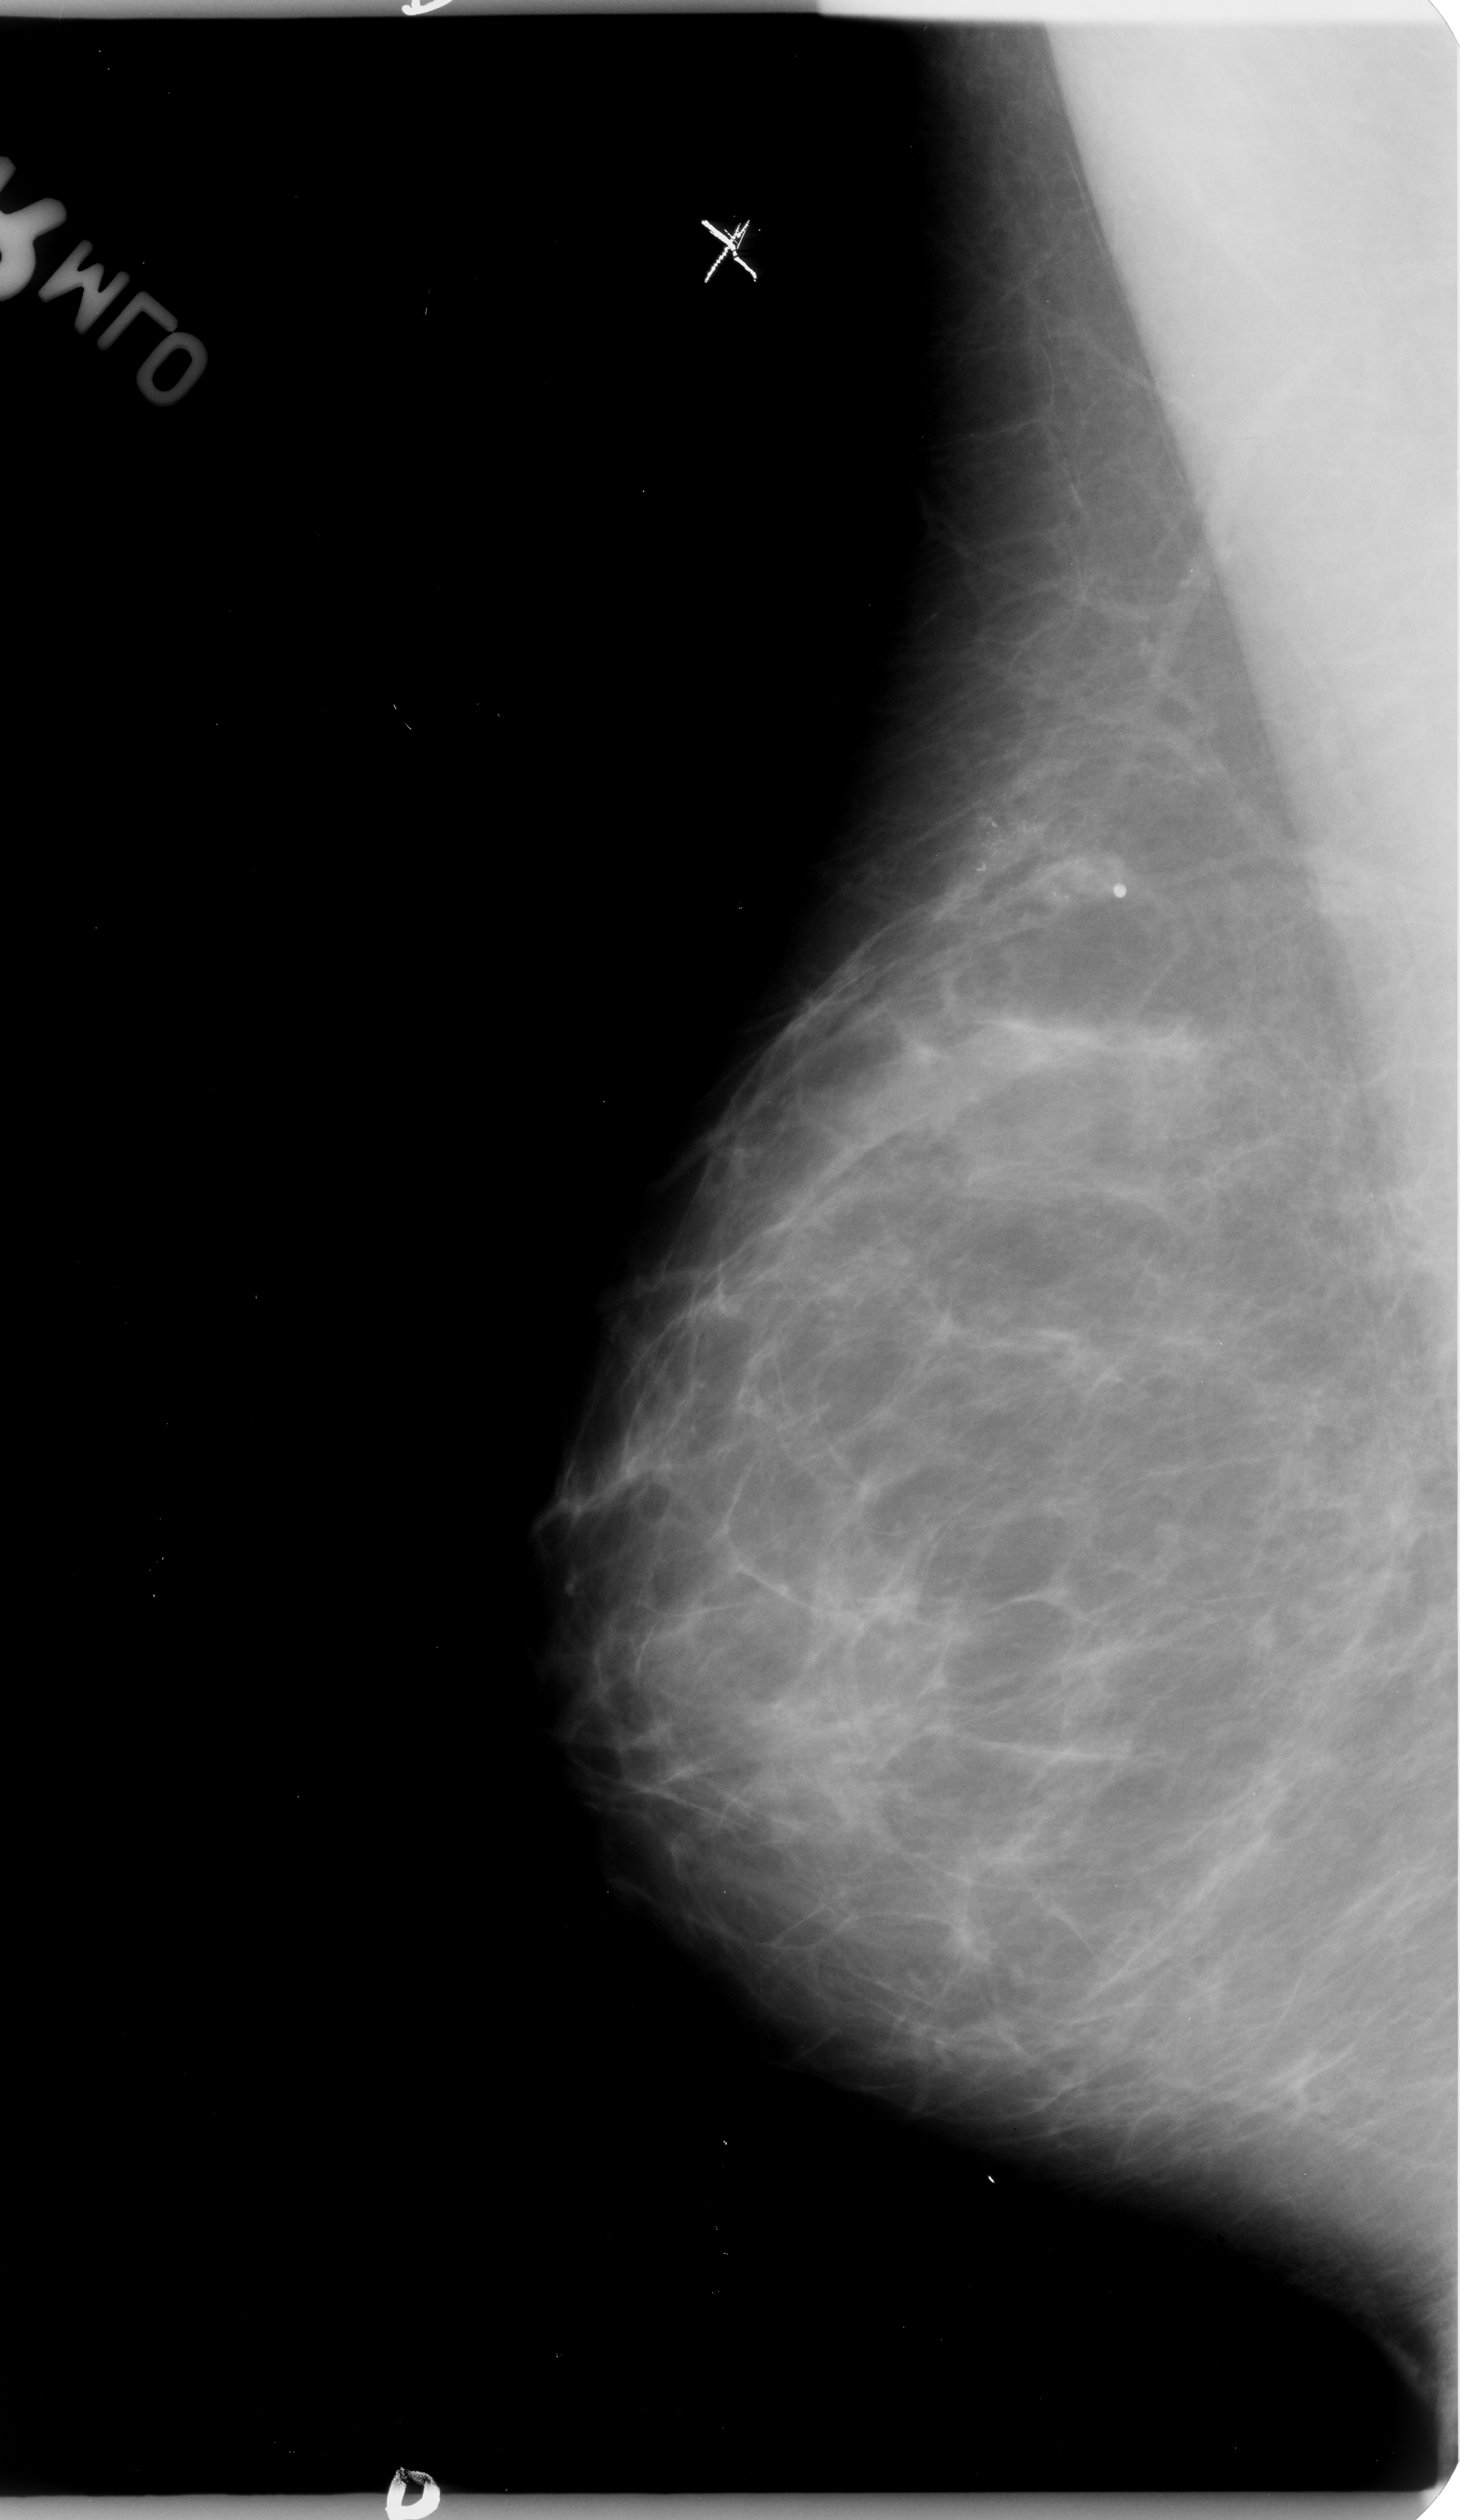
Mammogram (digitized film), right breast, MLO view, BI-RADS breast density category 2 (scale 1–4).
Radiologist-marked abnormalities on this image: calcifications, morphology pleomorphic, distribution clustered; BI-RADS assessment category 4; pathology result (as recorded, not read from the image): malignant.